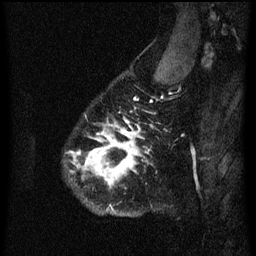
Breast MRI (dynamic contrast-enhanced), one sagittal slice; position 53 of 60 along the scan axis; dynamic contrast-enhanced series, image 2 of 3 at this slice position (ordered by acquisition); 1.5 T; TE 4.2 ms, TR 8.4 ms; 2 mm slice thickness; 256 × 256 image matrix, field of view 180 × 180 mm. Patient: female, 34 years. From the clinical record (not read from this slice): setting: breast cancer imaged before/during neoadjuvant chemotherapy; receptor status: HR-positive, HER2-negative.
Annotated regions visible in this slice (semi-automatically segmented with operator editing):
- analysis volume of interest (the breast-tissue region the enhancement analysis was run in; not a lesion): bounding box [x1, y1, x2, y2] px = [72, 58, 173, 217]
- tumour enhancement mask (voxels above the 70 % enhancement threshold inside the analysis volume of interest): [72, 124, 141, 187]